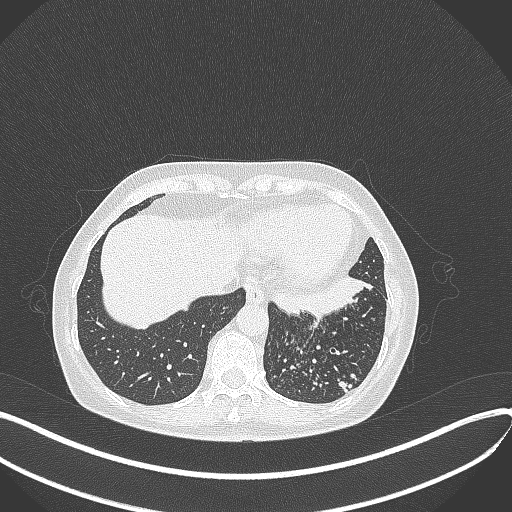
Chest CT, one axial slice; slice 98 of 429 in the series (ordered by position); reconstruction kernel B70f; 100 kVp; lung window (W 1500 / L -600 HU); 512 × 512 image matrix, field of view 400 × 400 mm. Patient: female, 63 years. Case-level facts recorded for this patient, not image findings: clinical TNM (as recorded): T1b N0 M0; histopathological grade: G2-3.
Outlined on this slice (bounding box drawn by a radiologist):
- lung tumour (recorded histology: adenocarcinoma): box from (x=275, y=275) to (x=373, y=317) px